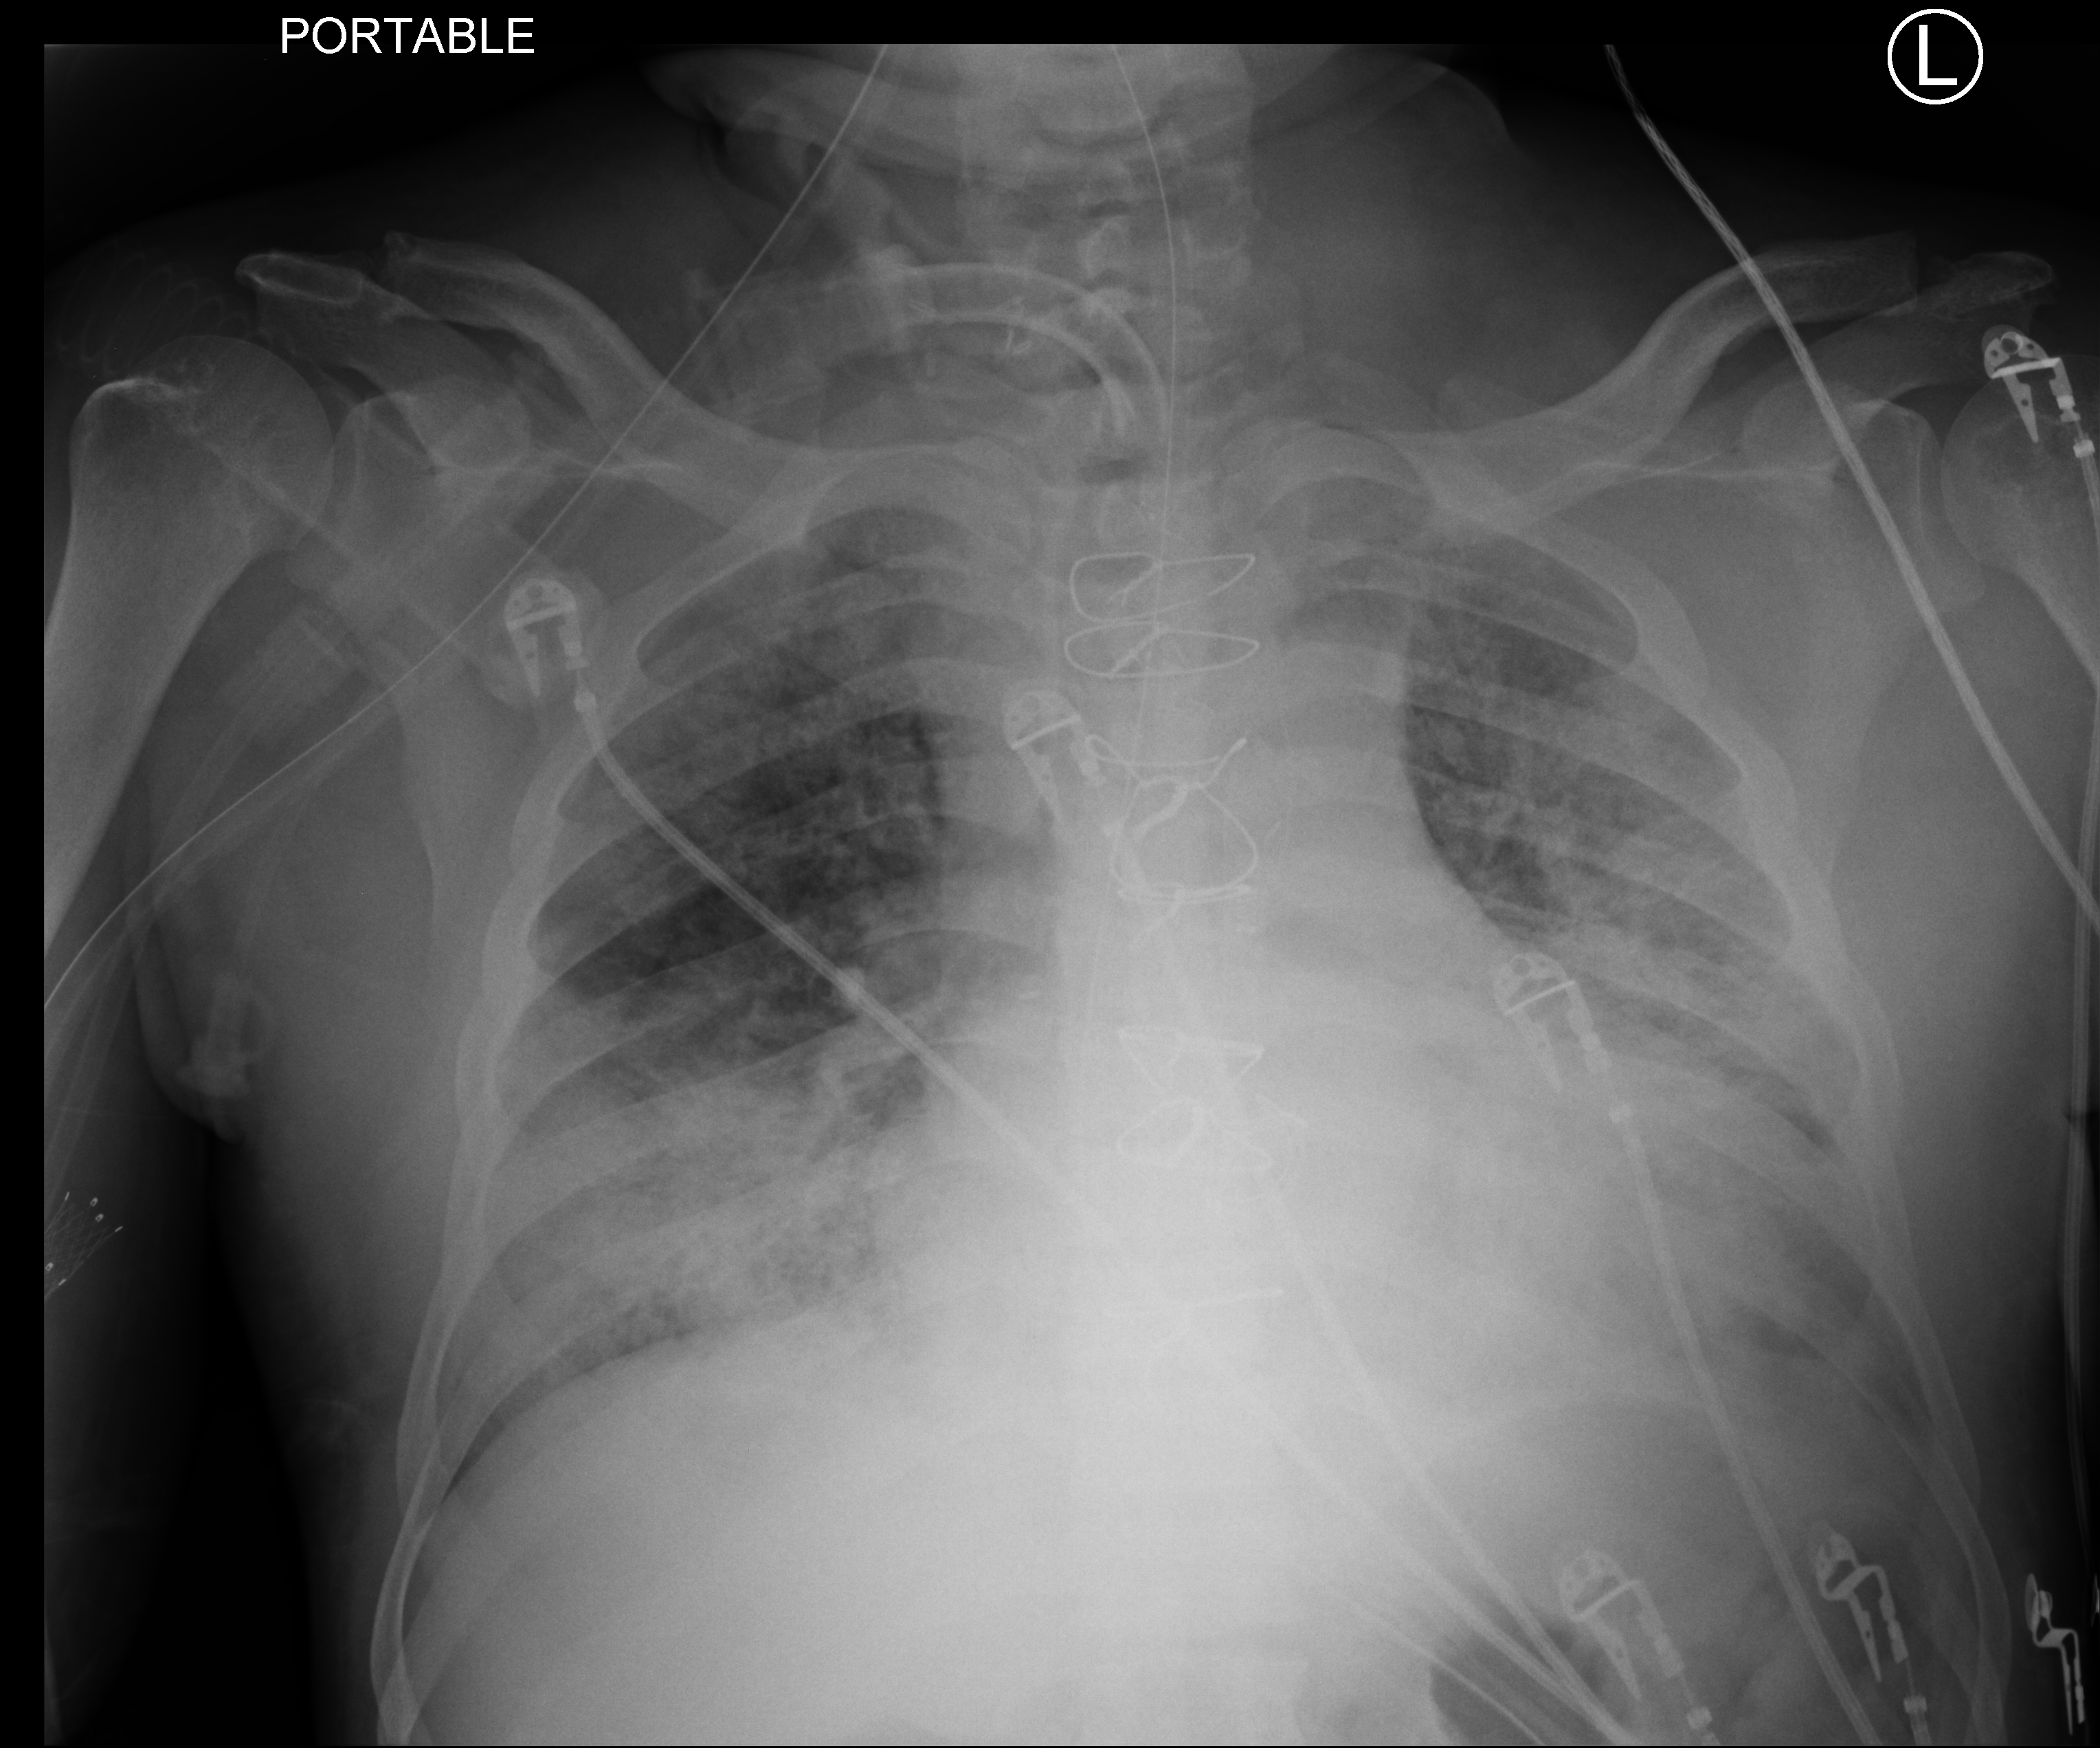
Bedside chest radiograph (computed radiography). Patient hospitalised with COVID-19; male, aged 60–74 years.
Hospital-stay facts (about this admission, not read from this image; timing relative to this image not recorded):
- admitted to intensive care during this hospital stay: yes
- smoking status (admission record): never